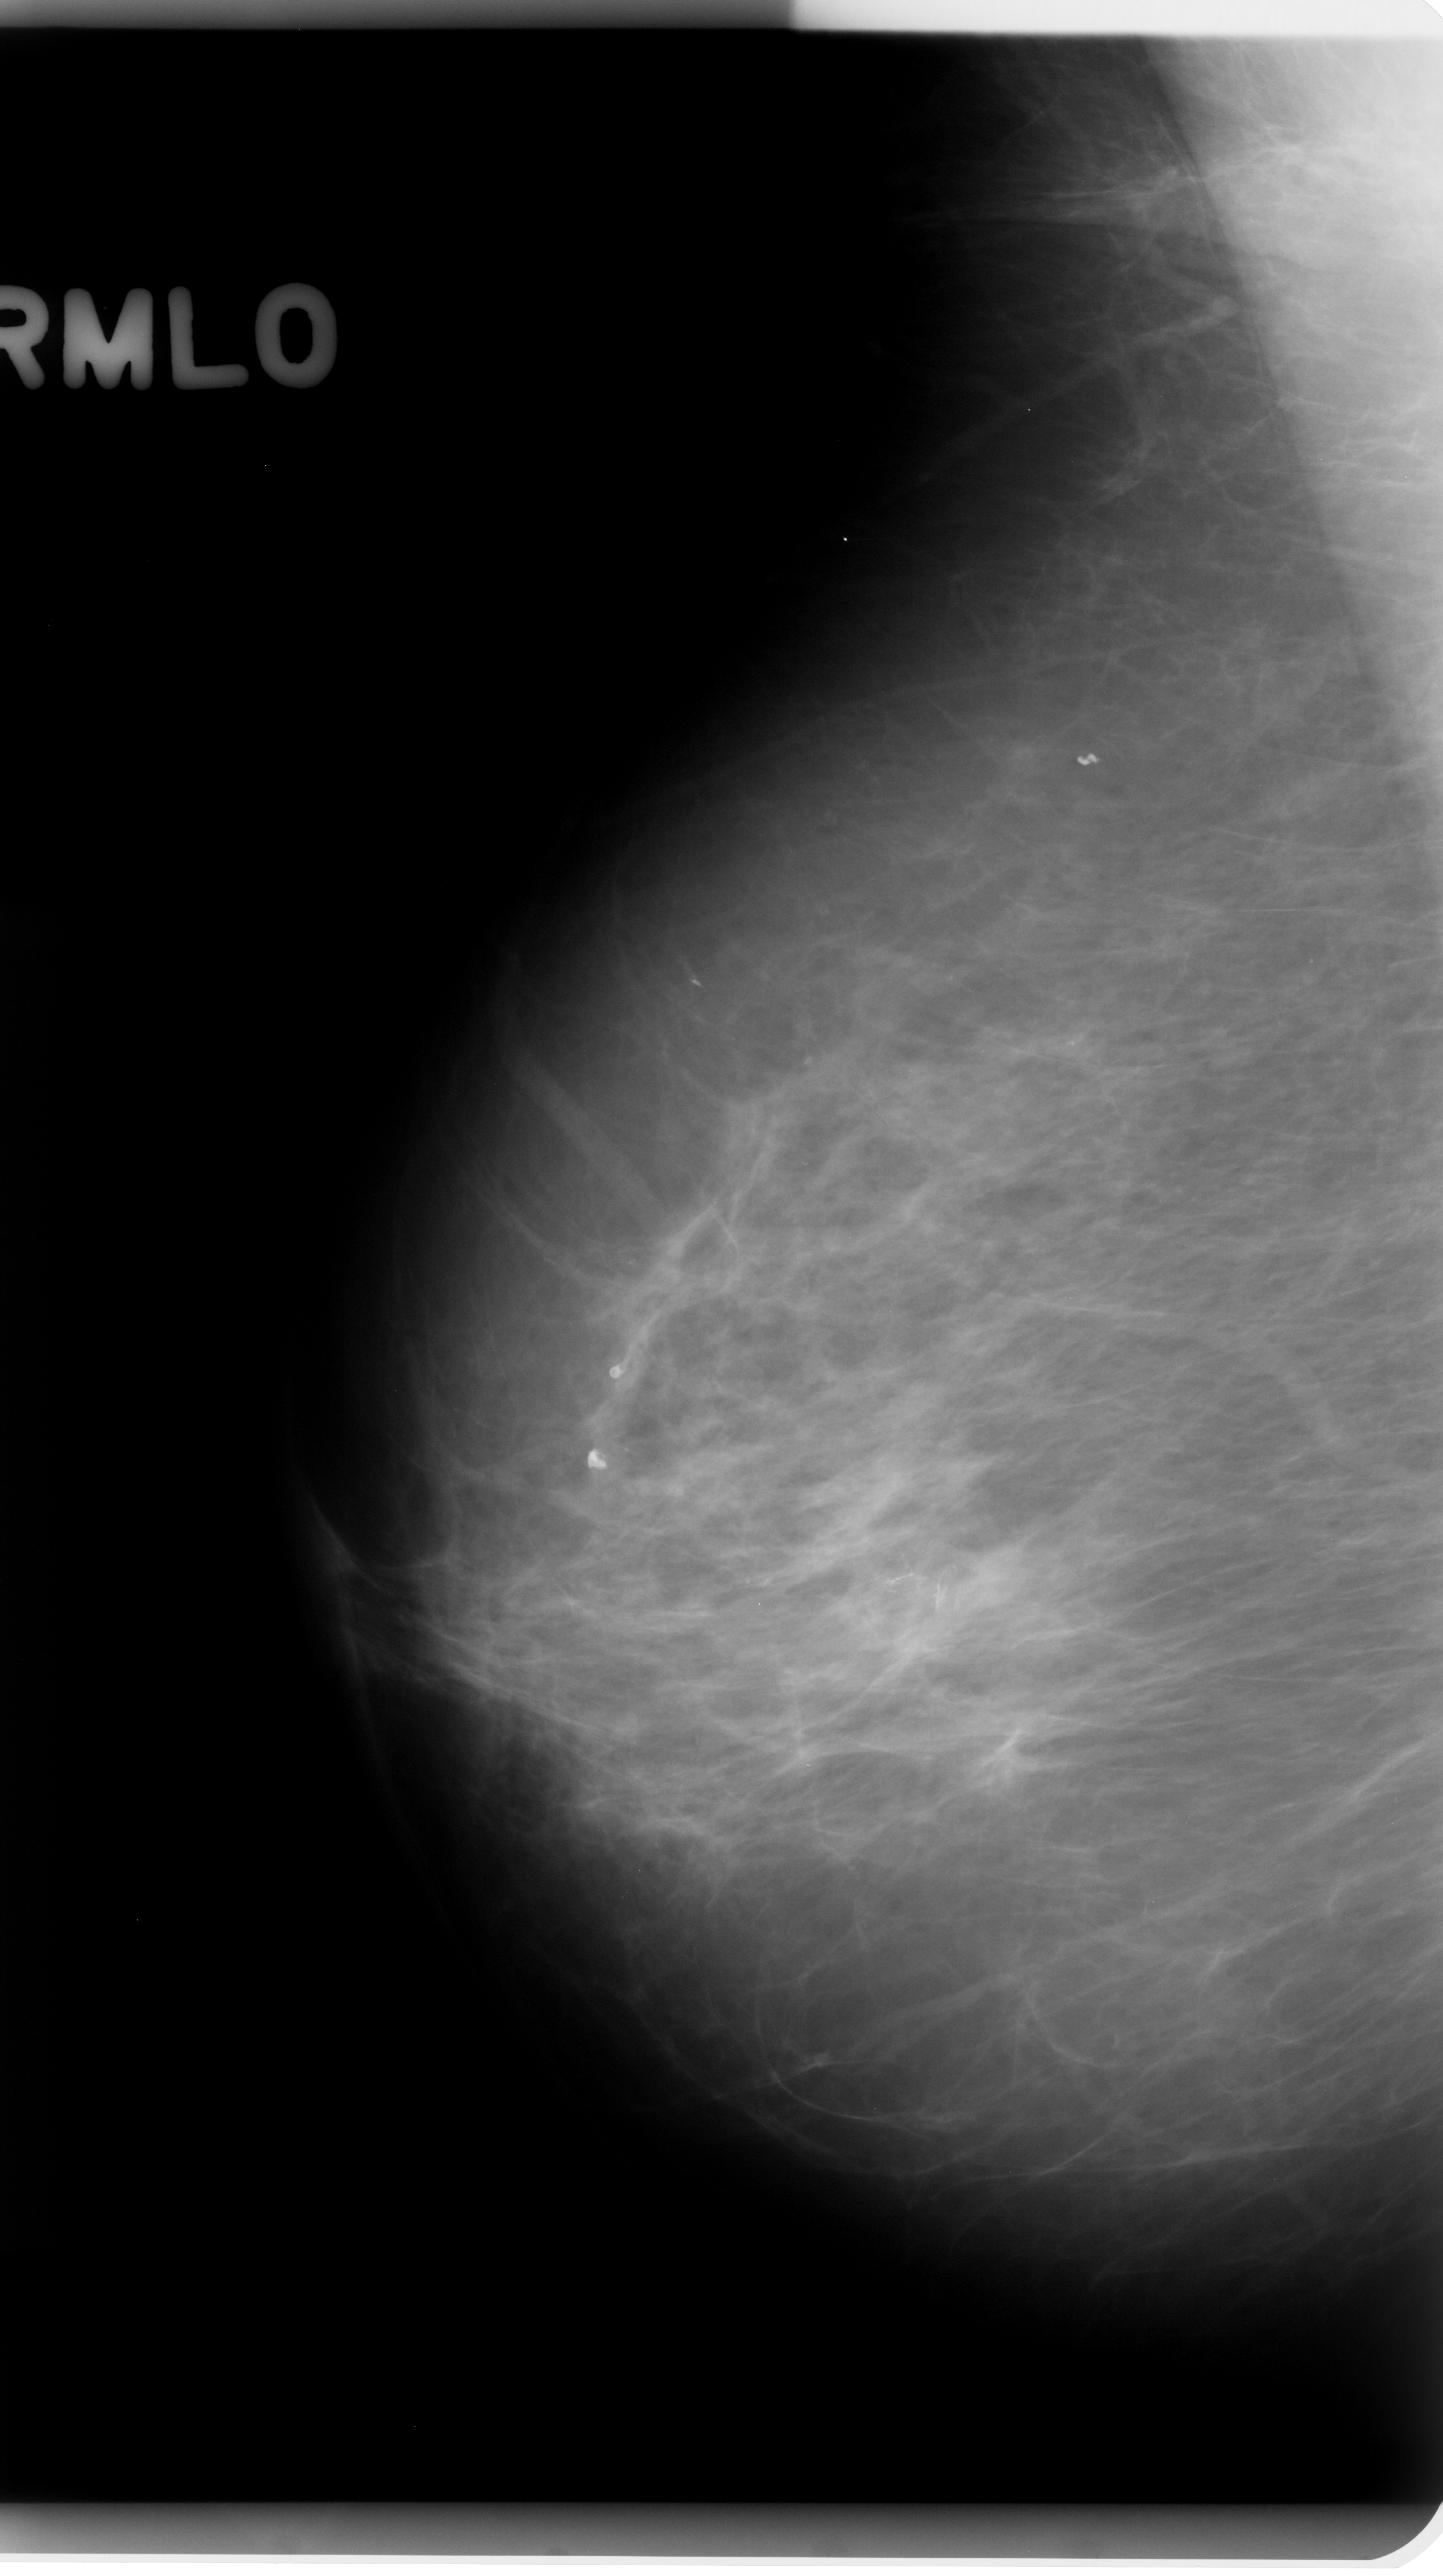
Scanned film-screen mammogram, right breast, mediolateral oblique (MLO) view, breast composition: scattered fibroglandular densities (BI-RADS density category 2 of 4).
Marked findings (only marked abnormalities are described; nothing is implied about the rest of the image): calcifications, morphology fine linear branching, distribution clustered; BI-RADS assessment category 4; subtlety rating 5 on a 1 (subtle) to 5 (obvious) scale; pathology (as recorded): benign.